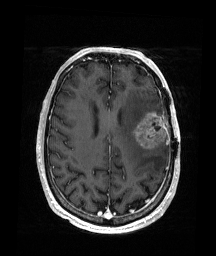
Brain MRI from a brain-tumour surgery series, one axial slice; position 68 of 176 along the scan axis; T1-weighted post-contrast; 216 × 256 image matrix, field of view 219 × 260 mm. Case-level facts recorded for this patient, not image findings: histopathology: Glioblastoma; WHO grade: 4; IDH mutation: no; tumour location: Left Frontal.
Structures marked on this image (manually delineated by an expert):
- tumour: bounding box [x1, y1, x2, y2] px = [132, 111, 168, 149]